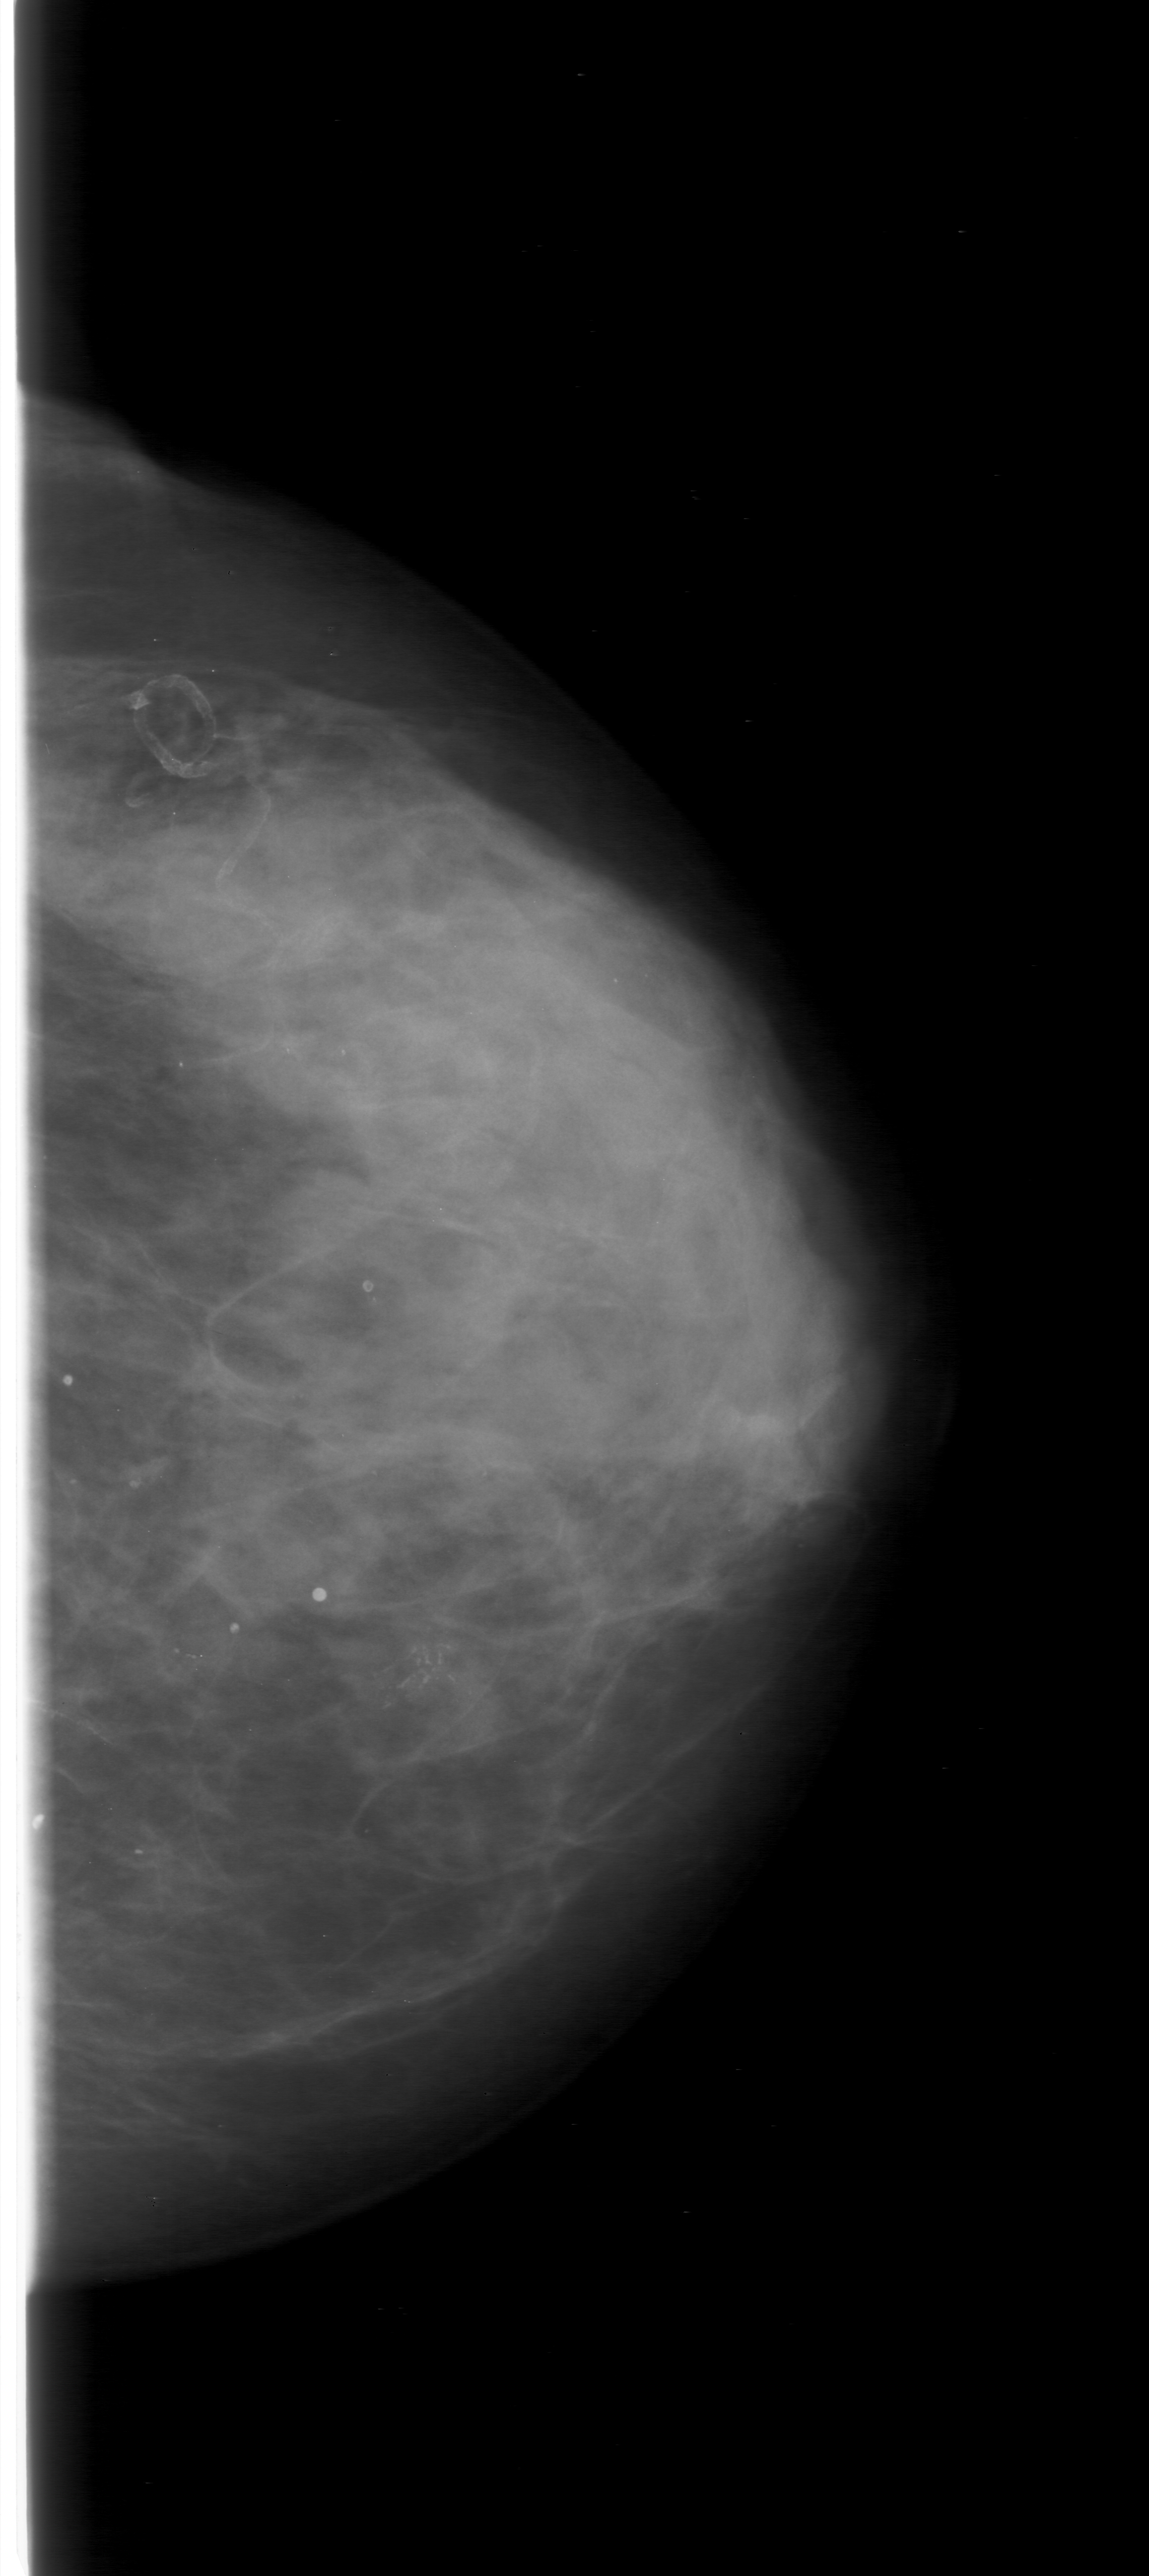
Digitized screen-film mammogram, left breast, CC view, BI-RADS breast density category 3 (scale 1–4).
Marked findings (only marked abnormalities are described; nothing is implied about the rest of the image): calcifications, morphology fine linear branching, distribution clustered; BI-RADS assessment category 5; pathology (as recorded): malignant.